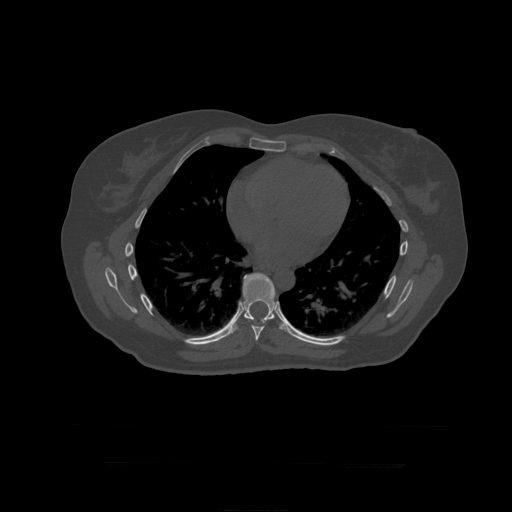
CT including the spine, one axial slice; position 271 of 399 along the scan axis; bone window (W 1800 / L 400 HU); 1.25 mm slice thickness; 512 × 512 image matrix, field of view 450 × 450 mm. Patient age 41 years. From the clinical record (not read from this slice): primary cancer: breast.
Annotated regions visible in this slice (semi-automatically segmented with operator editing):
- T8 vertebra: bounding box <251,325,265,341> (left, top, right, bottom; pixels)
- T9 vertebra: <229,273,291,336>